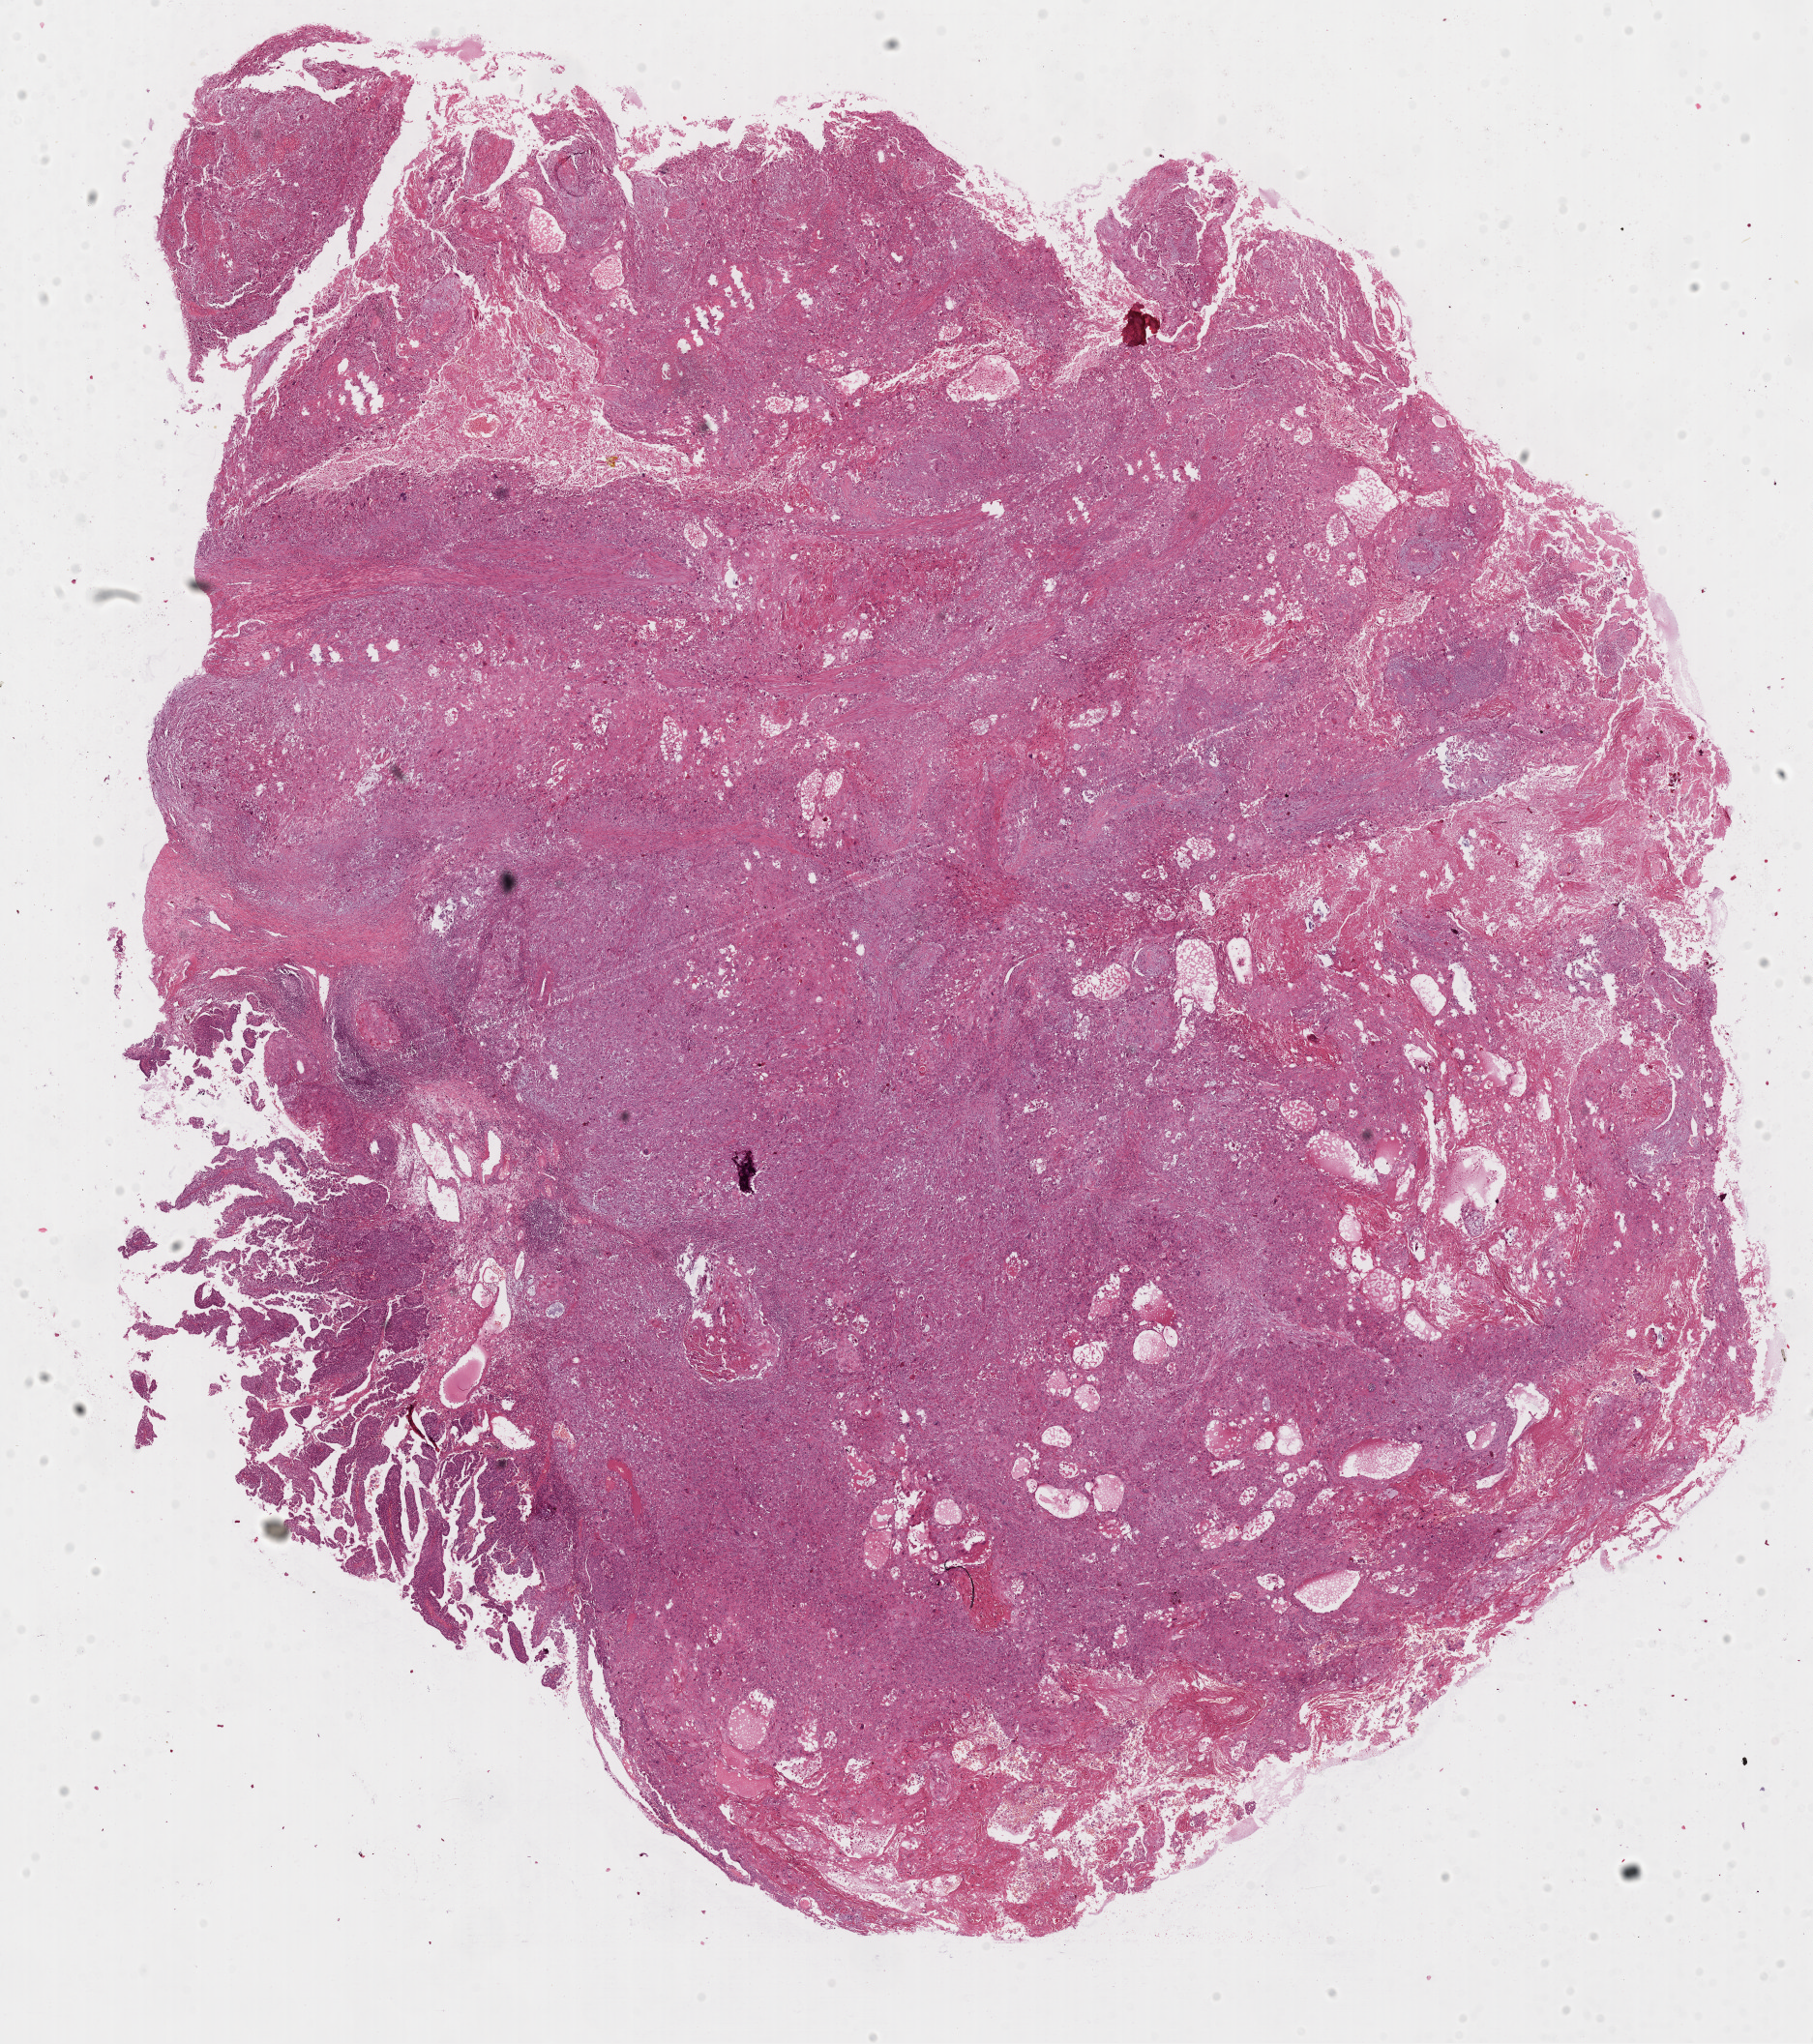
Whole-slide histology image, H&E-stained, whole scanned area (about 14.8 x 16.7 mm) shown as a low-resolution overview, formalin-fixed paraffin-embedded (FFPE) diagnostic section, sample: primary tumour, bladder. Female, age 75 years at initial diagnosis.
Pathologic diagnosis: Squamous cell carcinoma, NOS.